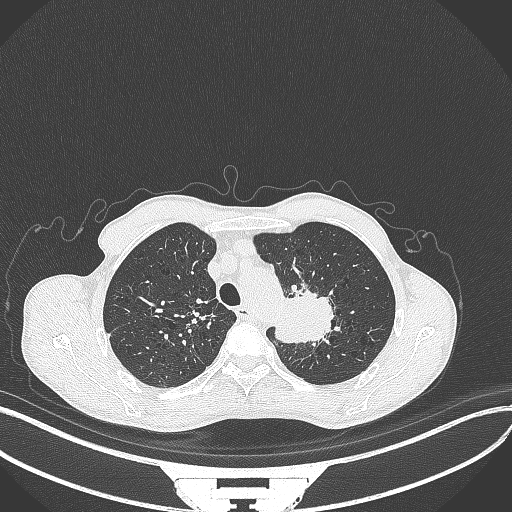
Chest CT, one axial slice. Position 335 of 386 along the scan axis. Reconstruction kernel B70f. 120 kVp. Lung window (W 1500 / L -600 HU). 1 mm slice thickness. 512 × 512 image matrix, field of view 400 × 400 mm. Patient: male, 65 years. Case-level facts recorded for this patient, not image findings: clinical TNM (as recorded): T2b N0 M0; histopathological grade: G2.
Structures marked on this image (rectangle marked by the reading radiologist):
- lung tumour (recorded histology: adenocarcinoma): bounding box <270,281,341,345> (left, top, right, bottom; pixels)